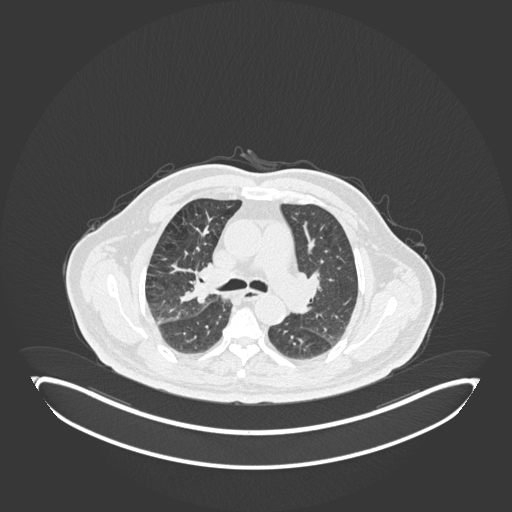
Chest CT, one axial slice; position 113 of 247 along the scan axis; reconstruction kernel B30f; 120 kVp; lung window (W 1500 / L -600 HU); 512 × 512 image matrix, field of view 500 × 500 mm. Male patient, age 72 years. From the clinical record (not read from this slice): clinical TNM (as recorded): T1c N0 M0.
Annotated regions visible in this slice (bounding box drawn by a radiologist):
- lung tumour (recorded histology: squamous cell carcinoma): bounding box <186,259,215,309> (left, top, right, bottom; pixels)